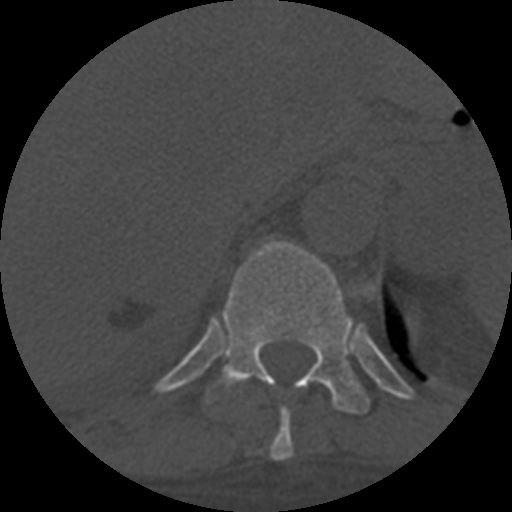
CT including the spine, one axial slice. Position 343 of 708 along the scan axis. 120 kVp. One of 3 acquisitions stored at this slice position. Bone window (W 1800 / L 400 HU). 512 × 512 image matrix, field of view 160 × 160 mm. Patient age 55 years. Case-level facts recorded for this patient, not image findings: primary cancer: colon; vertebrae with lytic lesions (as recorded): T12, L1, L5.
Outlined on this slice (semi-automatic segmentation, software-assisted and operator-edited):
- T10 vertebra: box from (x=270, y=408) to (x=293, y=461) px
- T11 vertebra: (x=207, y=240)–(x=369, y=415)